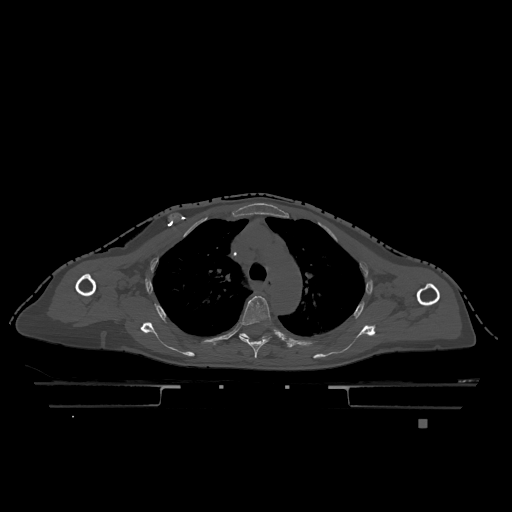
CT including the spine, one axial slice. Slice 870 of 1317 in the series (ordered by position). Bone window (W 1800 / L 400 HU). 0.5 mm slice thickness. 512 × 512 image matrix, field of view 500 × 500 mm. Female patient, age 74 years. Case-level facts recorded for this patient, not image findings: primary cancer: lung; vertebrae with lytic lesions (as recorded): T1, T4, T5, T6, L4, L5.
Outlined on this slice (semi-automatic segmentation, software-assisted and operator-edited):
- T4 vertebra: bounding box <239,296,271,358> (left, top, right, bottom; pixels)
- T5 vertebra: <240,333,267,339>